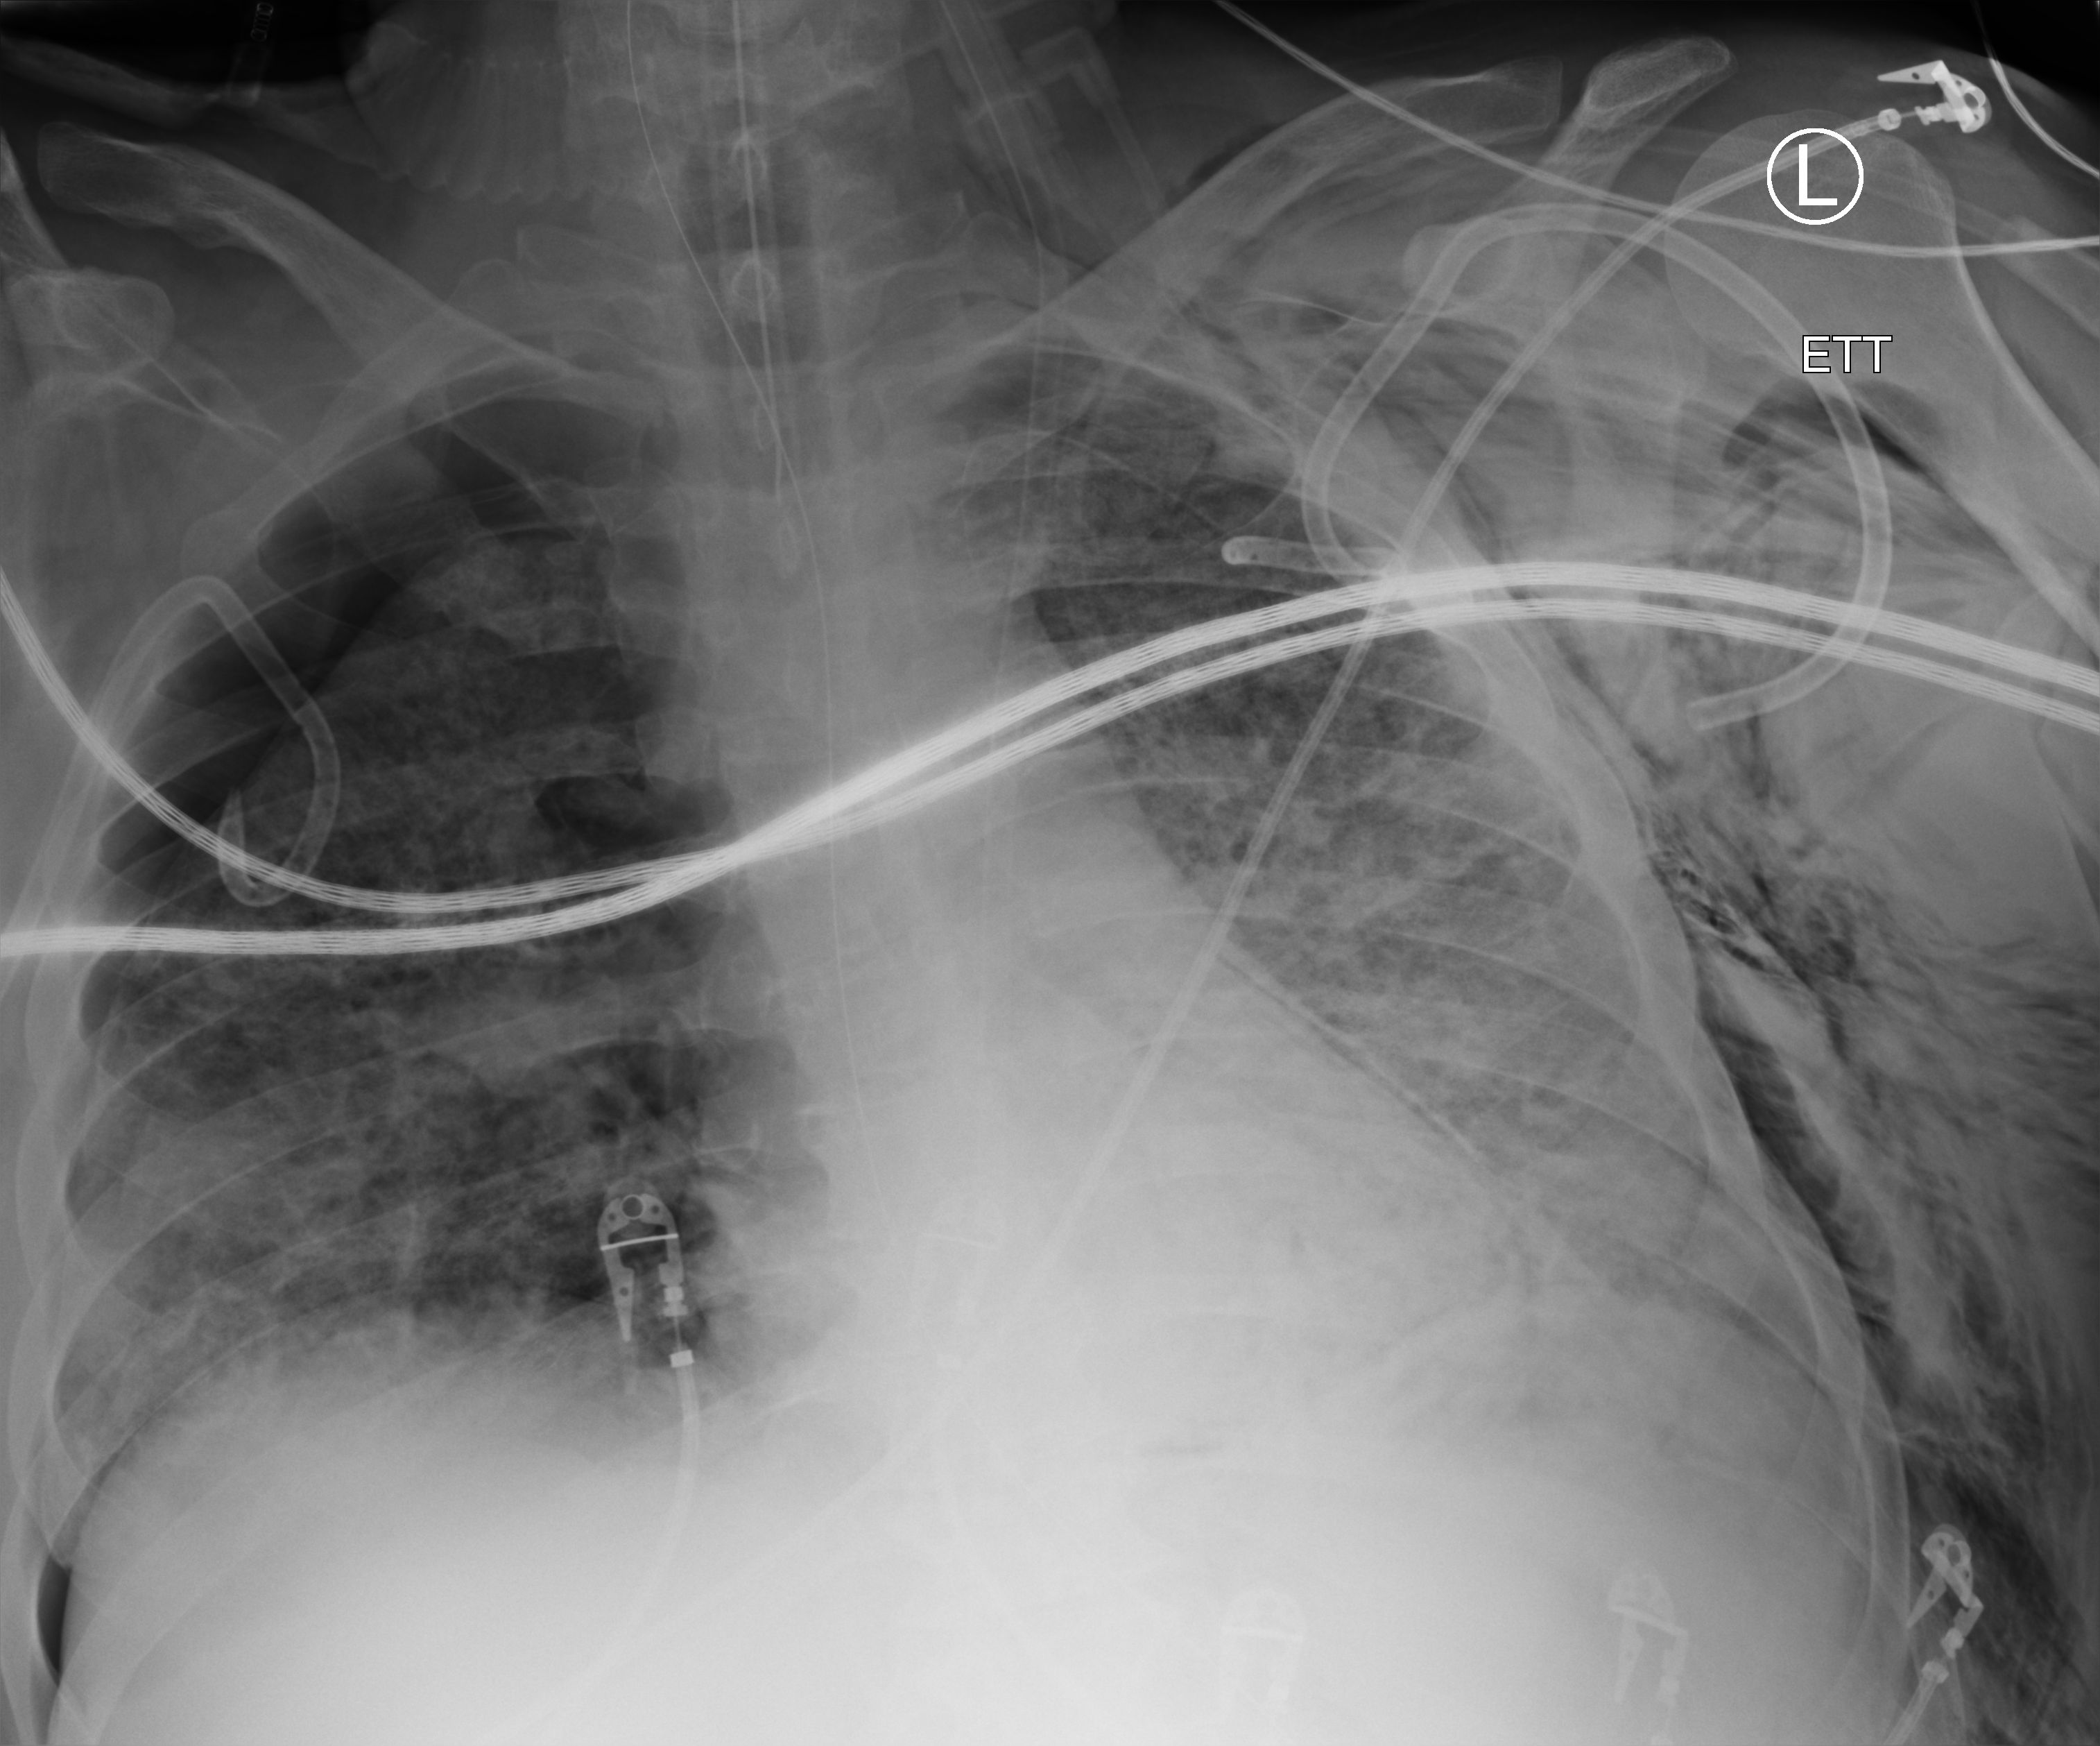
Chest X-ray (portable). Patient hospitalised with COVID-19, aged 18–59 years.
From the hospital-stay record, not from the radiograph (when in the stay this image was taken is not recorded):
- admitted to intensive care during this hospital stay: yes